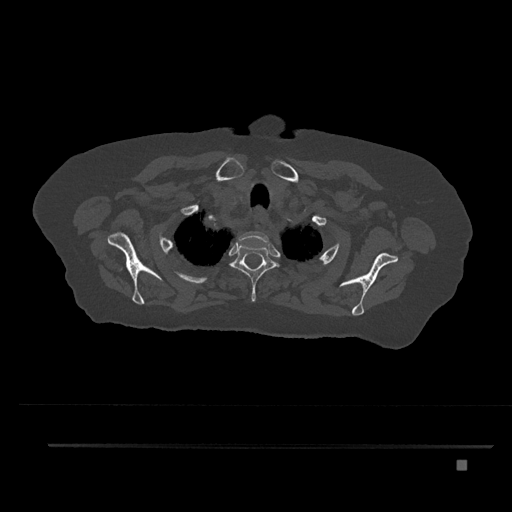
CT including the spine, one axial slice; position 671 of 797 along the scan axis; reconstruction kernel Br40s/3; bone window (W 1800 / L 400 HU); 0.5 mm slice thickness; 512 × 512 image matrix, field of view 437 × 437 mm. Female patient, age 76 years. Case-level facts recorded for this patient, not image findings: primary cancer: lung; vertebrae with lytic lesions (as recorded): T11, L3.
Structures marked on this image (semi-automatically segmented with operator editing):
- T1 vertebra: box from (x=238, y=231) to (x=269, y=246) px
- T2 vertebra: (x=230, y=242)–(x=280, y=302)